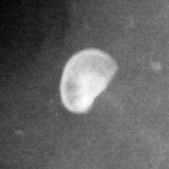
Crop from a digitized film mammogram around one marked abnormality, right breast, CC view.
- Calcifications, morphology round and regular / lucent center / punctate, distribution diffusely scattered; BI-RADS assessment category 2; benign without callback (not worked up further).